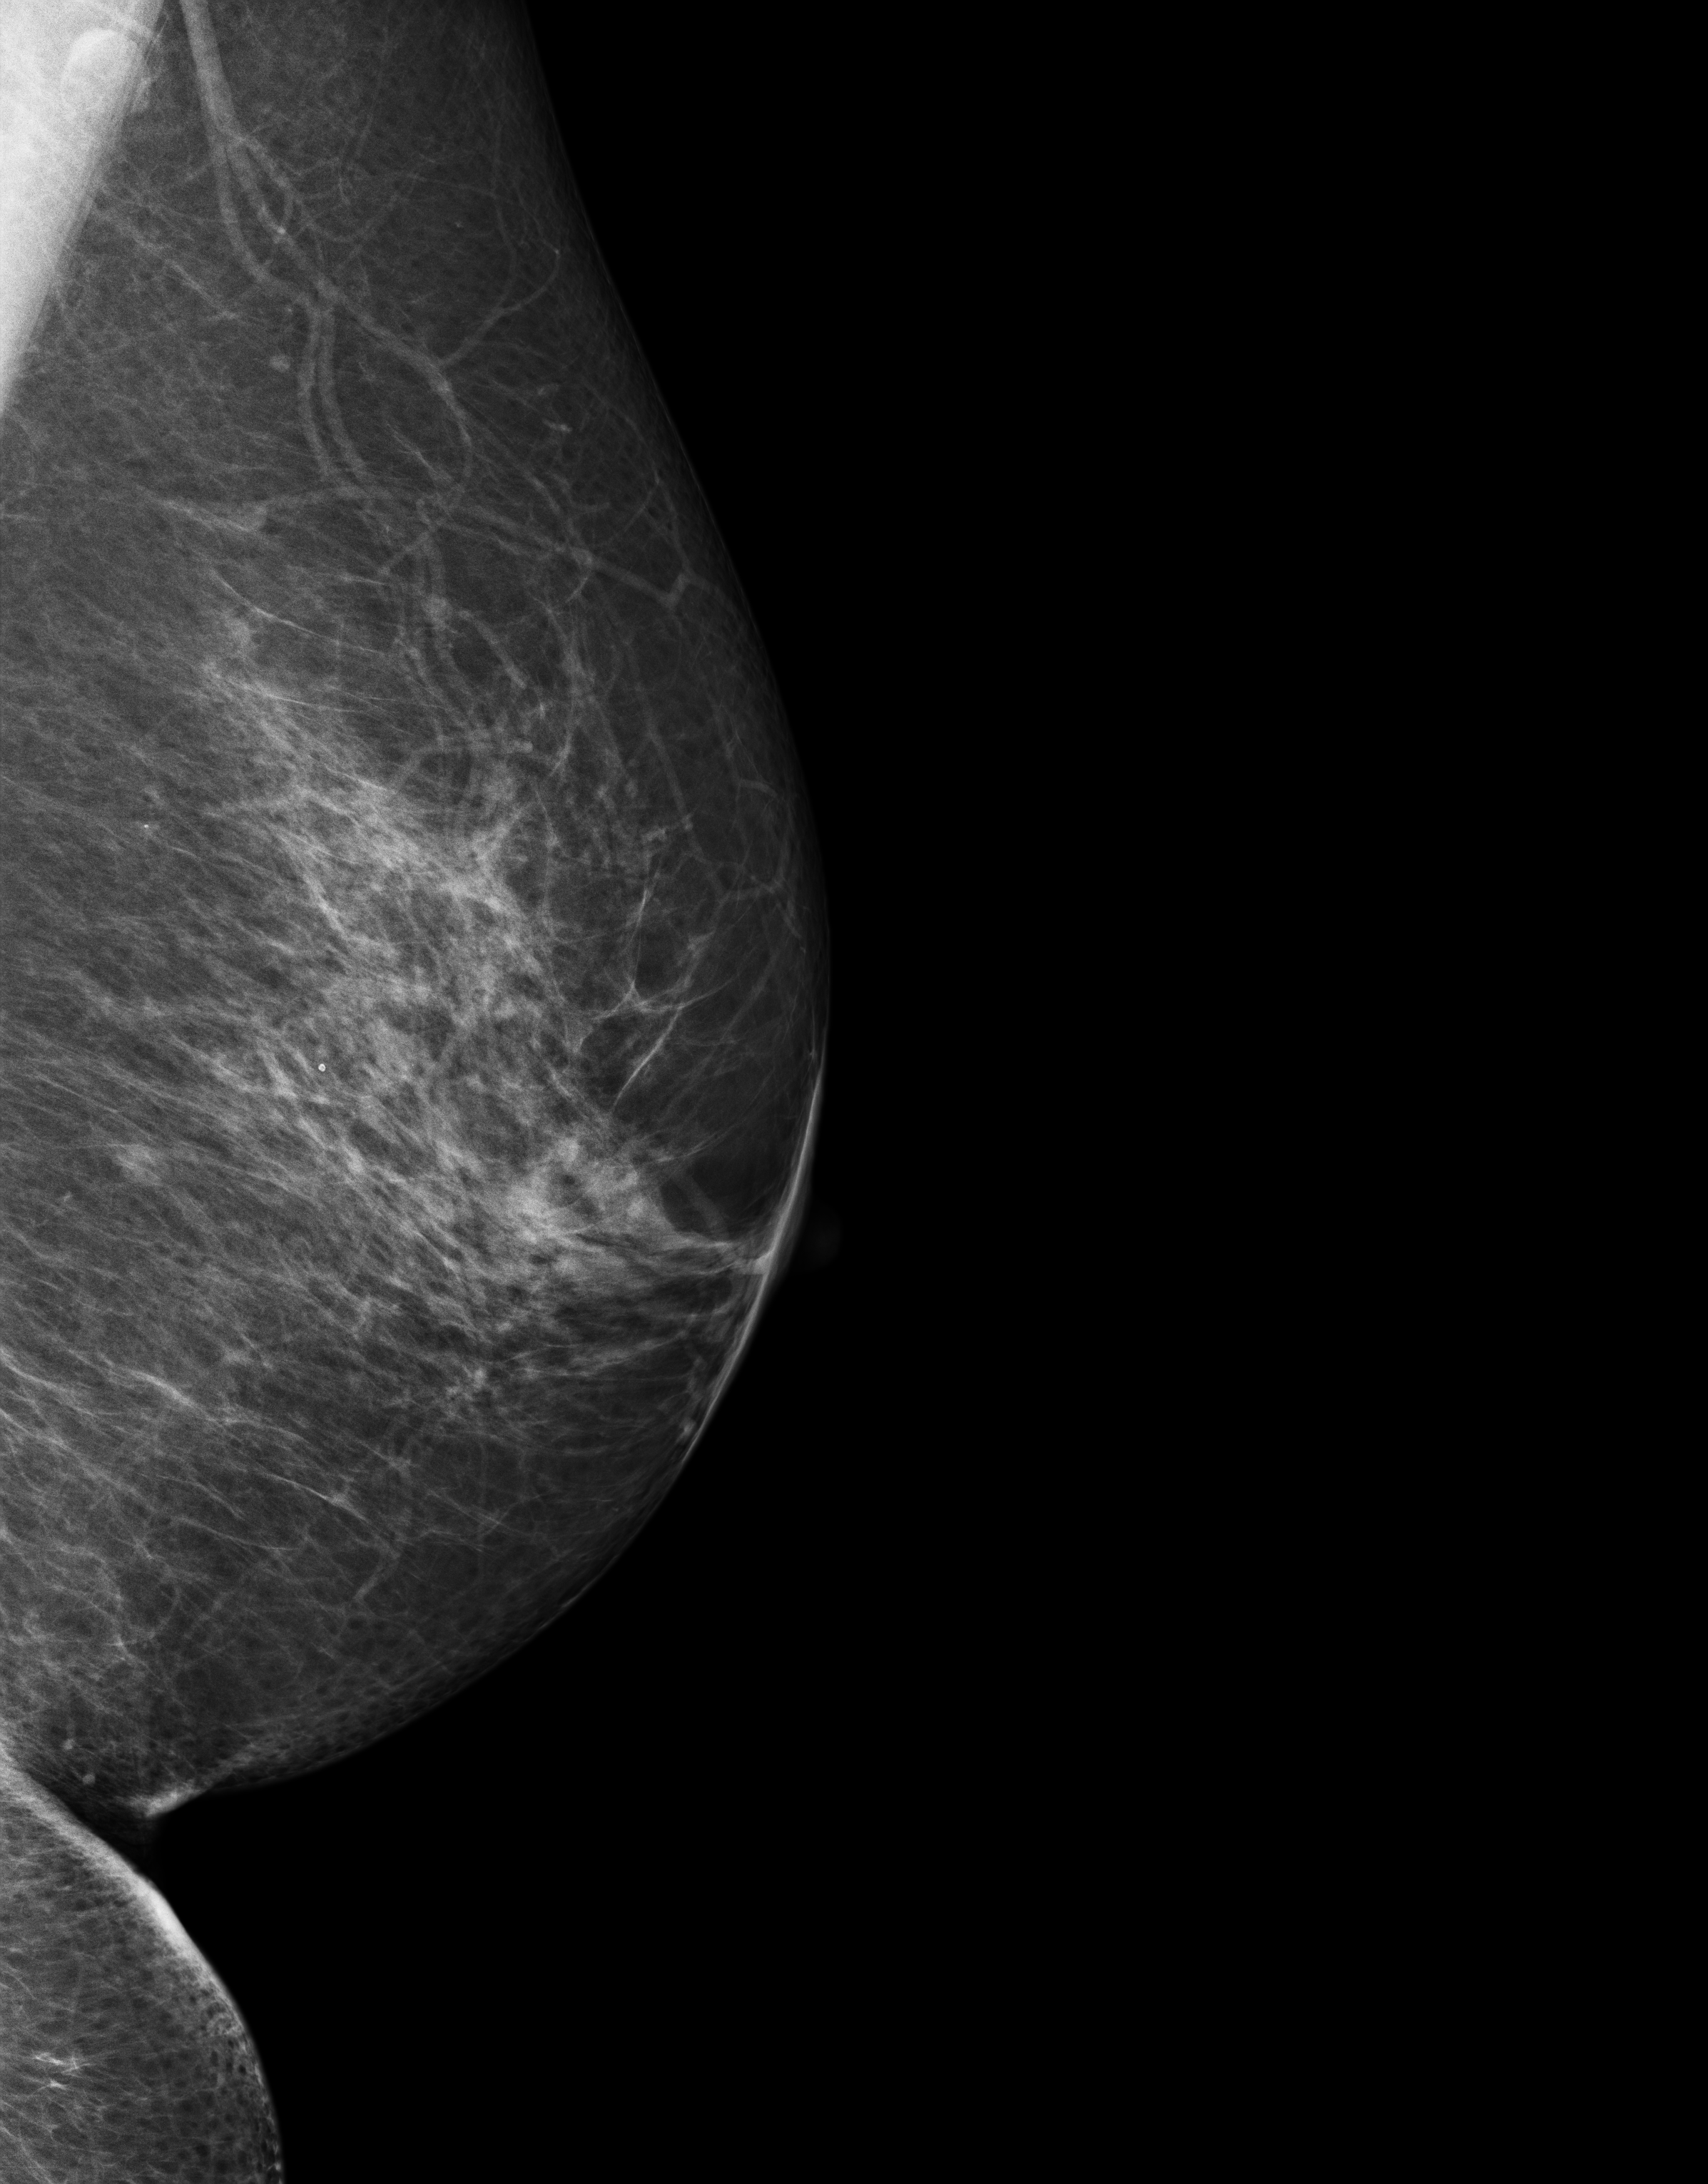
Full-field digital mammogram (FFDM); left breast; ML view; diagnostic examination (additional views); compressed breast thickness 85 mm; system: Senographe Essential ADS_56.21.3. Patient aged 53 years (female).
- BI-RADS breast density category at the screening exam (both breasts, scale 1–4): 3
- final BI-RADS category for the screening round (tomosynthesis exam, both breasts): category 4
- recall: recalled for additional imaging after this screen